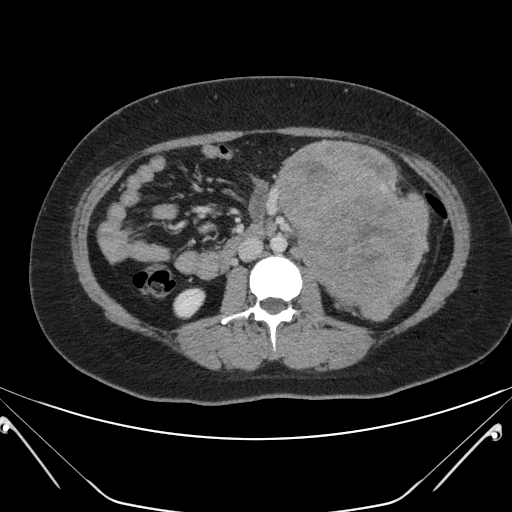
Contrast-enhanced abdominal CT, one axial slice. Position 99 of 168 along the scan axis. Intravenous contrast given. Soft-tissue window (W 400 / L 40 HU). 3 mm slice thickness. 512 × 512 image matrix, field of view 394 × 394 mm. Female patient, age 26 years. From the clinical record (not read from this slice): diagnosis: adrenocortical carcinoma; tumour side: left adrenal; tumour size at pathology: 28 cm; Ki-67 index: 20 %; stage (as recorded): 2.
Annotated regions visible in this slice (semi-automatically segmented with operator editing):
- mass: bounding box <279,143,426,318> (left, top, right, bottom; pixels)